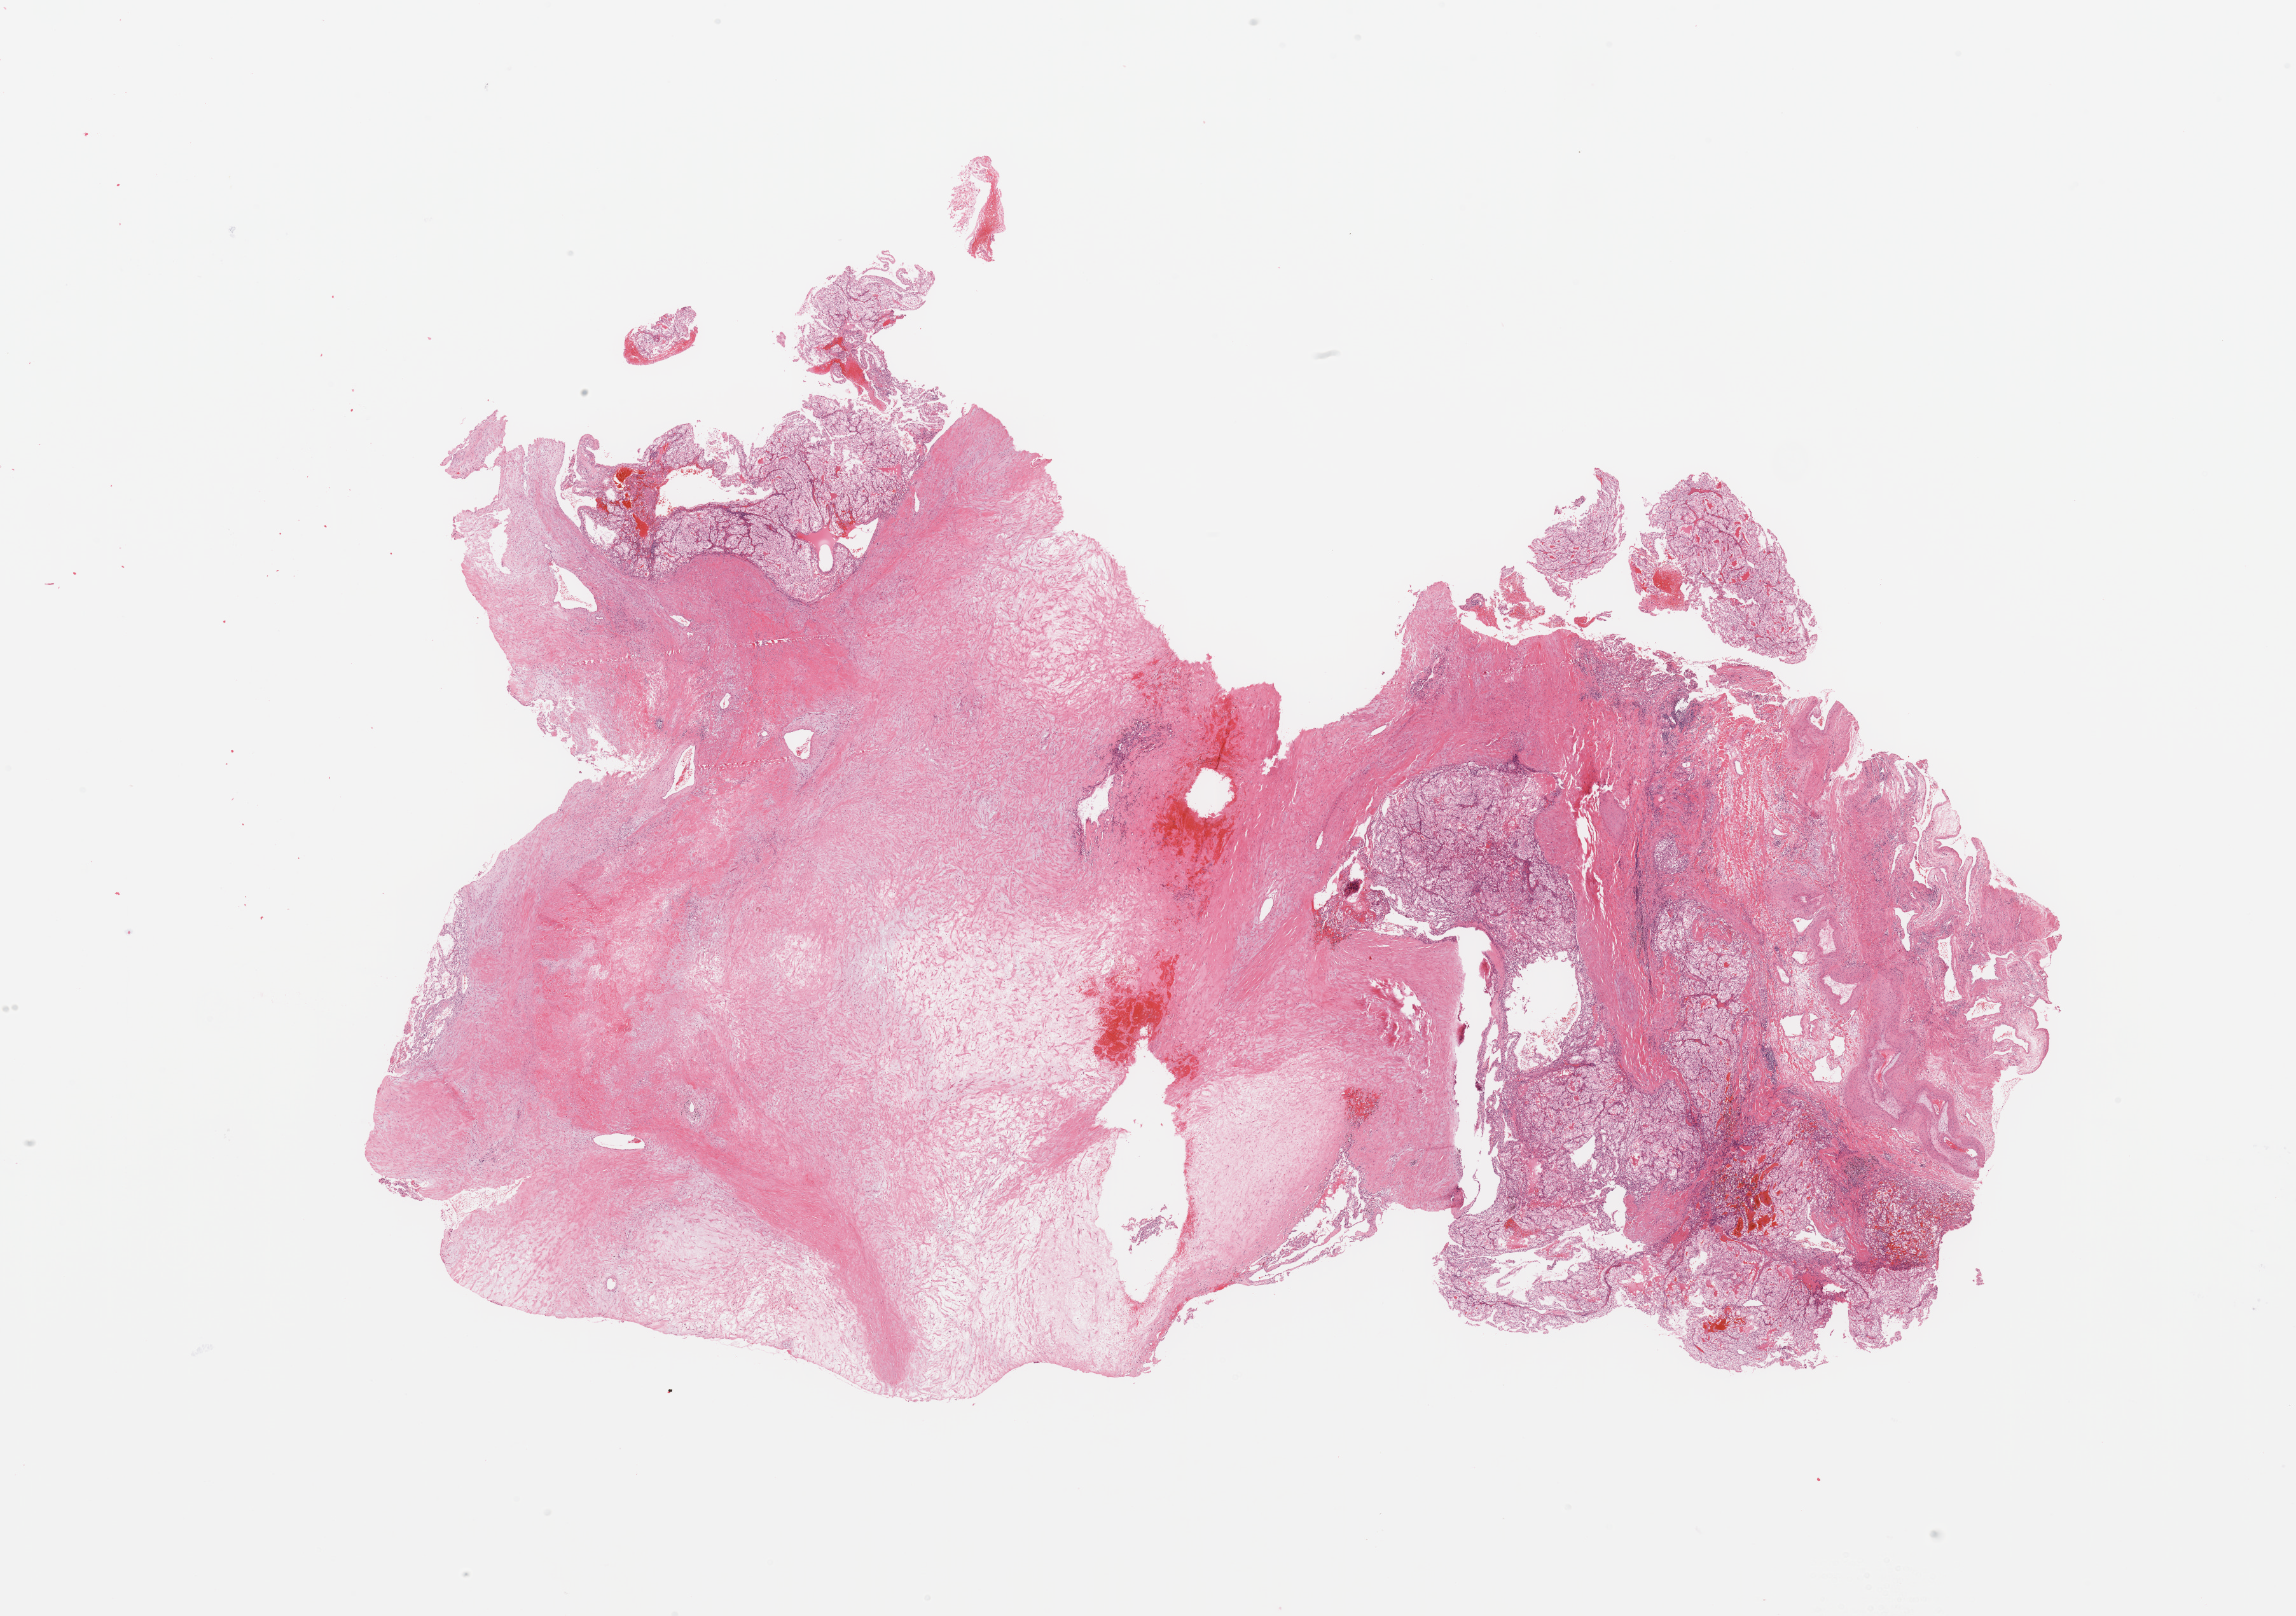
Digitized H&E-stained tissue section (whole slide), shown as a low-resolution overview of the whole scanned area (about 28.5 x 20.1 mm, slide scanned at 20x), kidney, tumour tissue. Female, 54 y/o. Histologic grade: G2 (moderately differentiated).
Histologic diagnosis: Renal cell carcinoma, NOS.